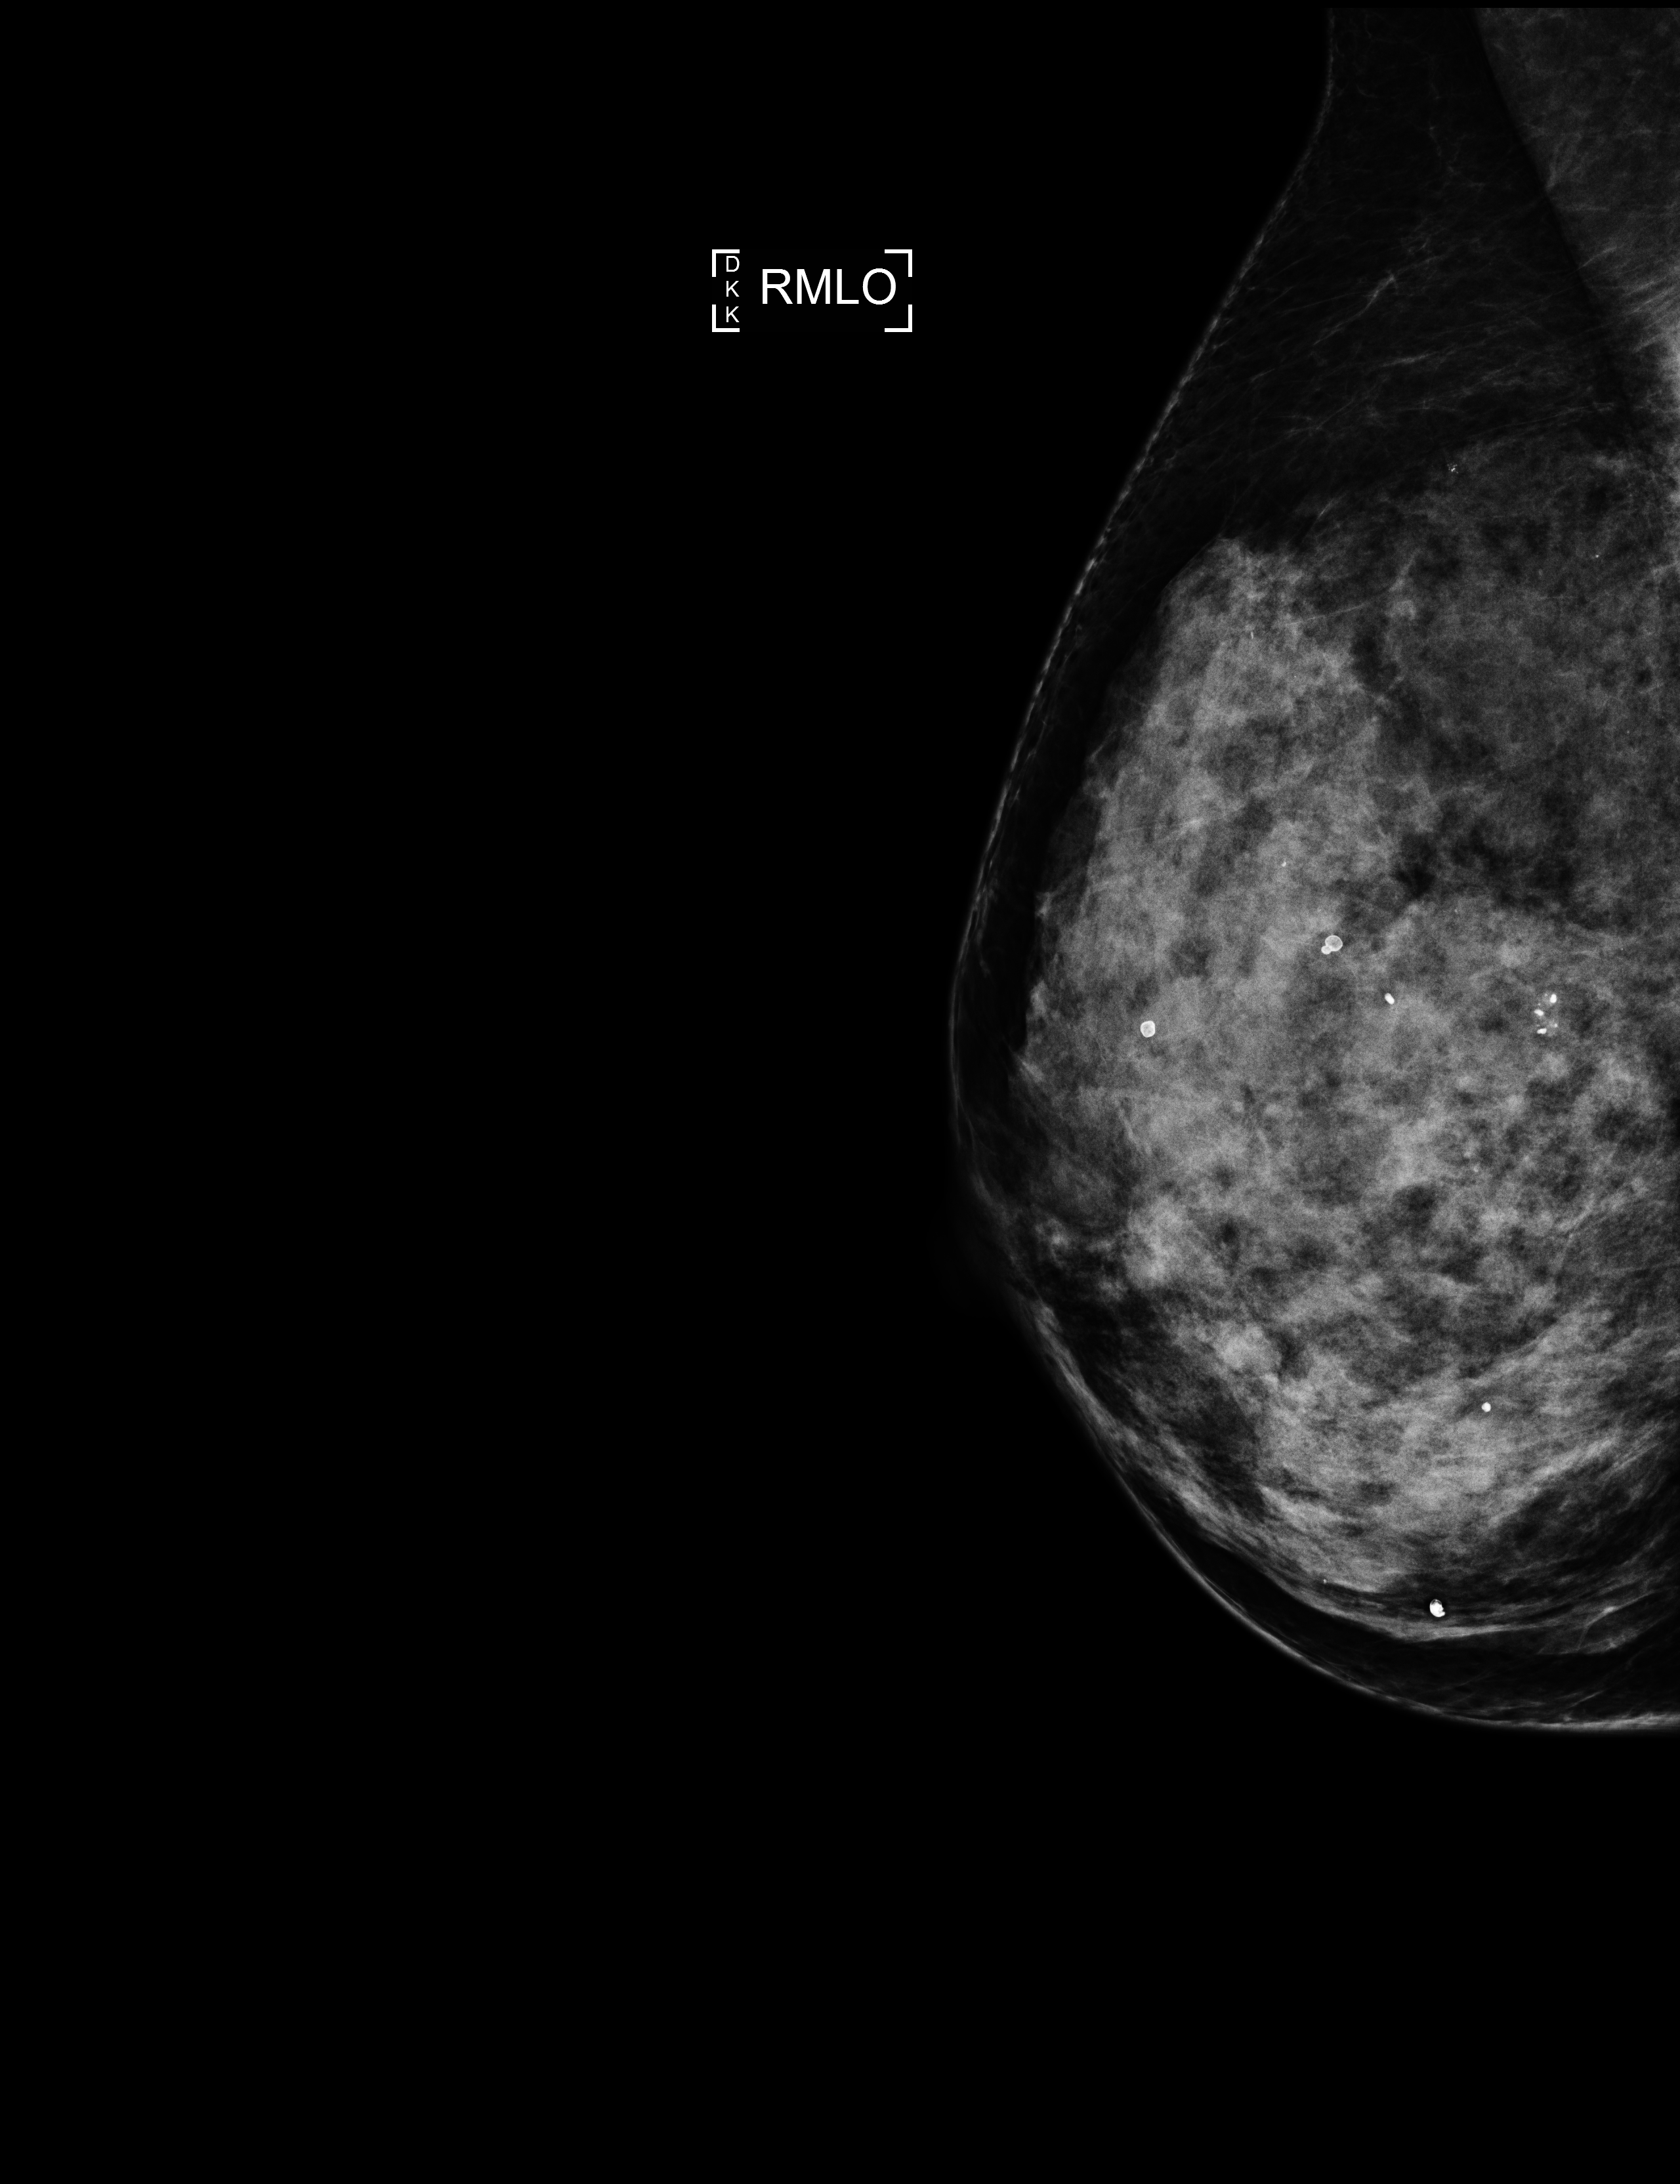
Annual screening mammography examination, compressed breast thickness 54 mm. Female patient, age 63 years.
Image type: full-field digital mammogram. Breast: right. Projection: mediolateral oblique (MLO) view.